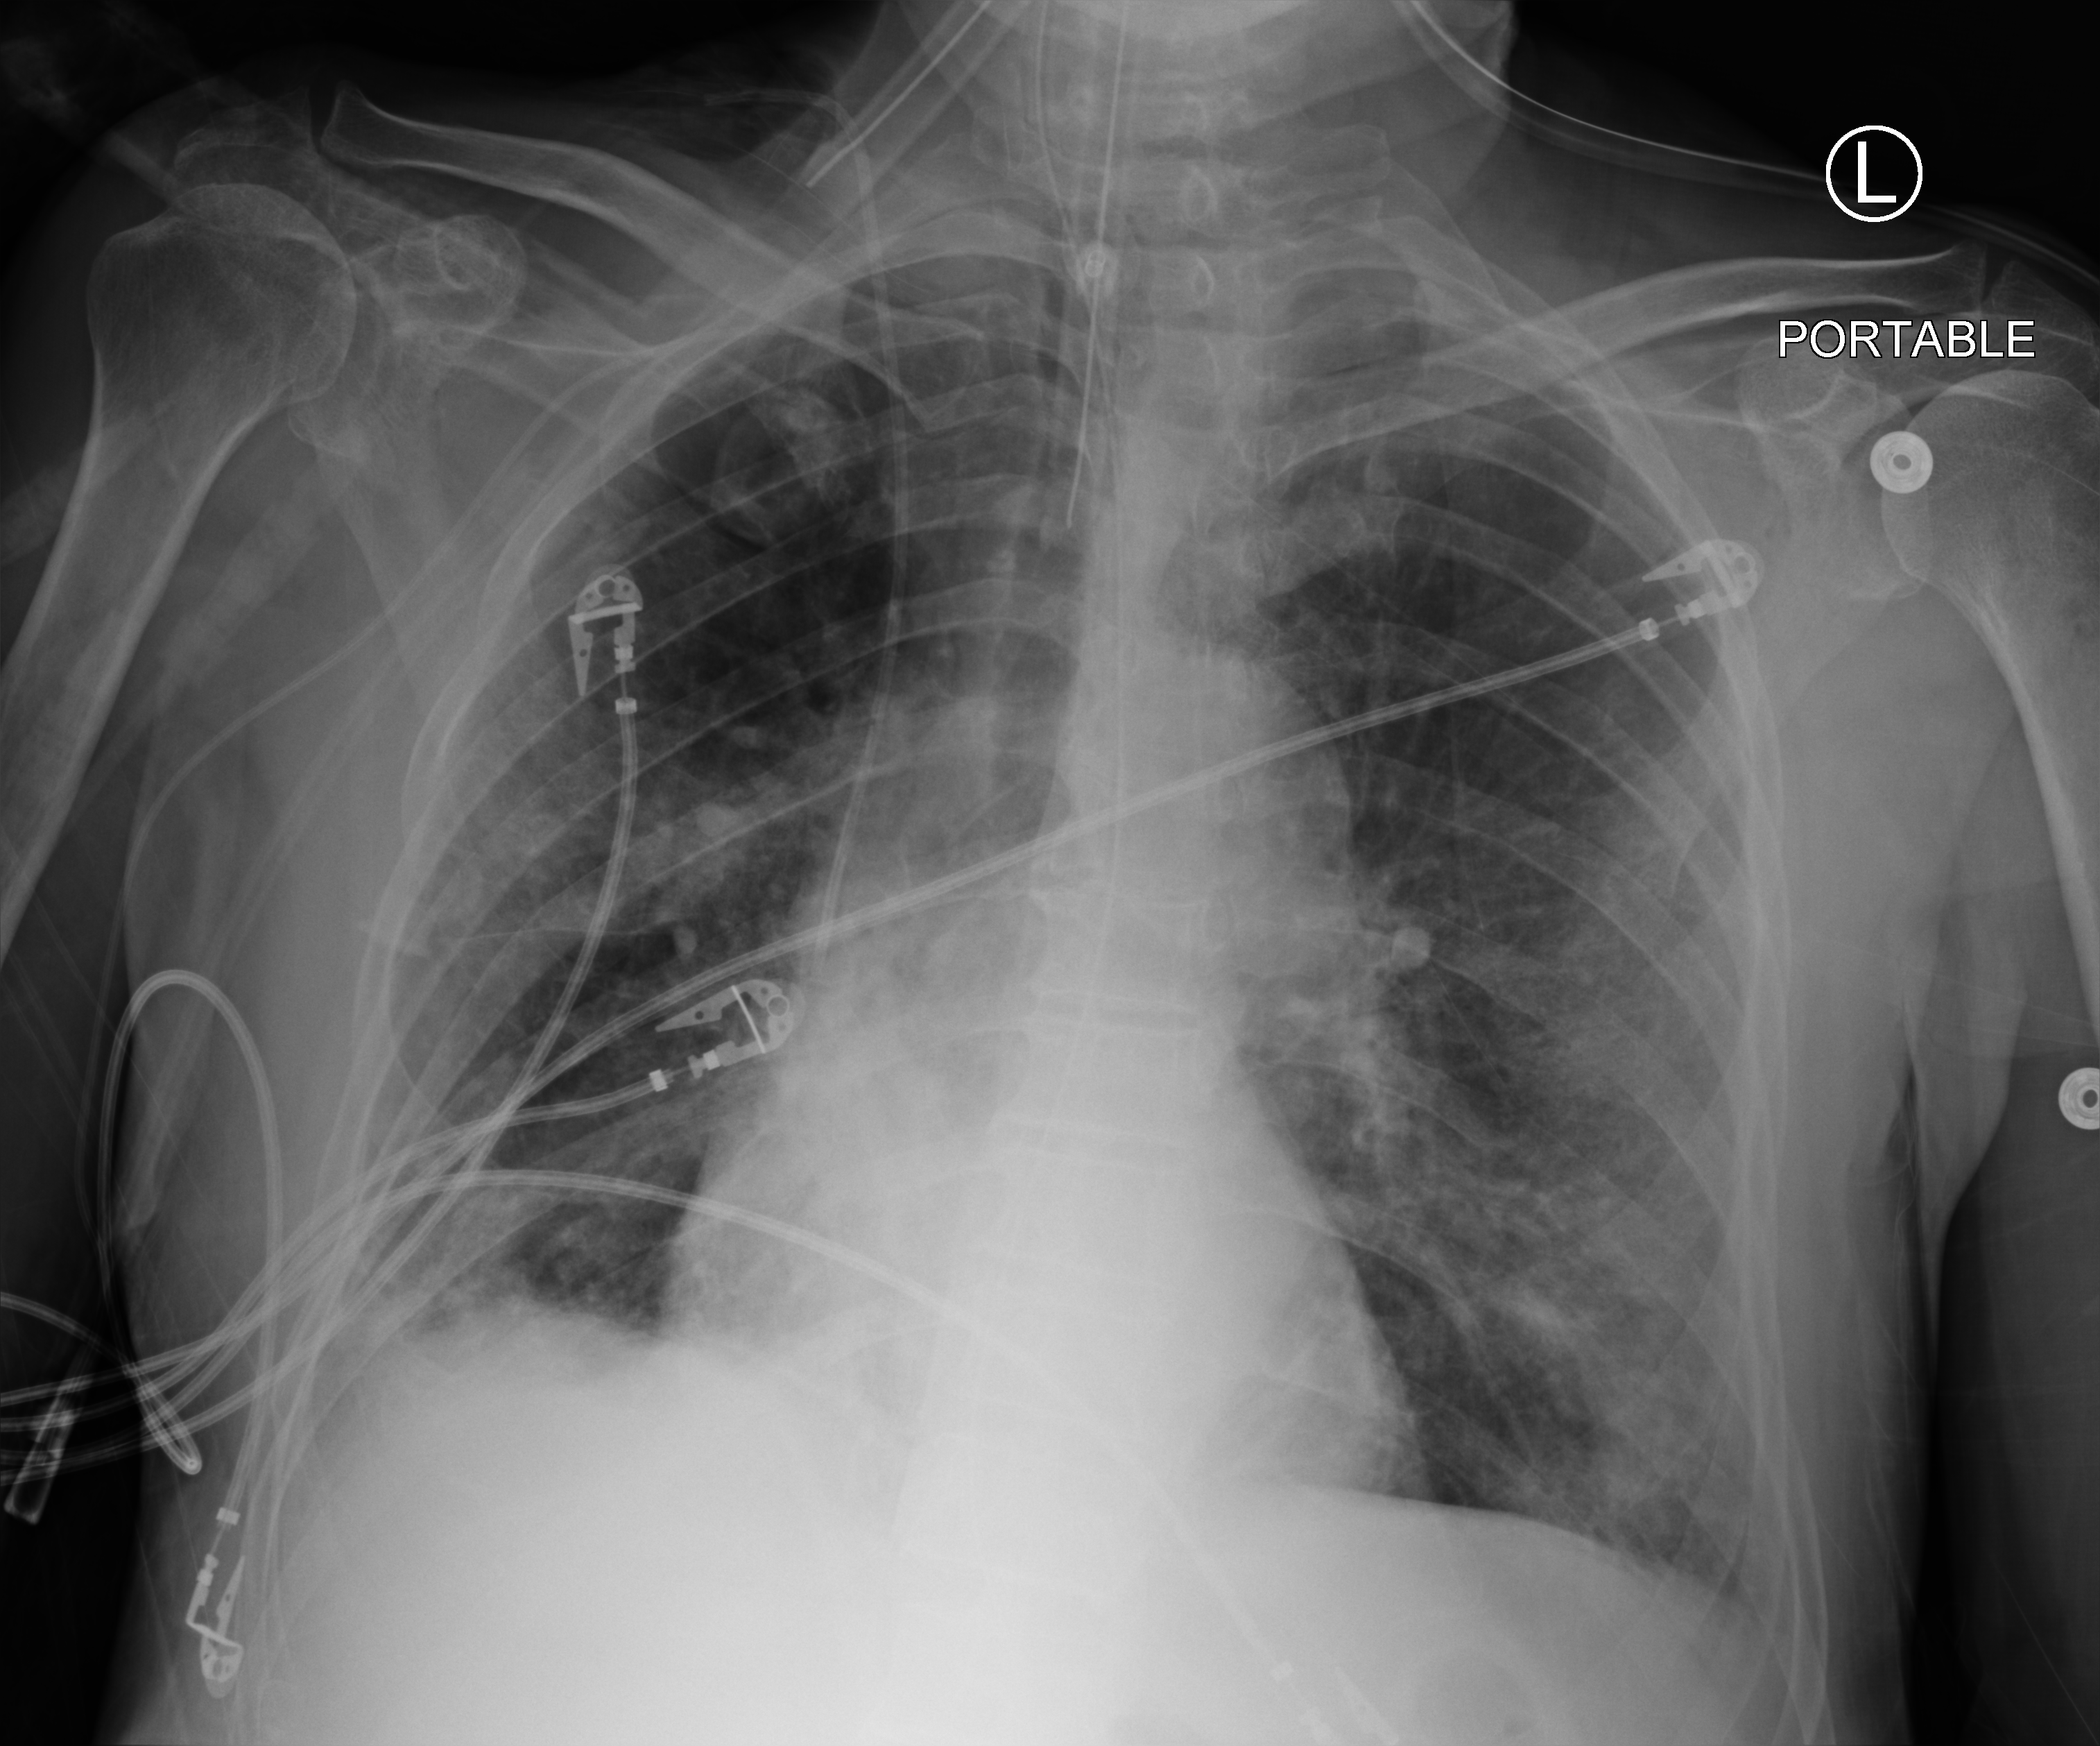
Chest X-ray (portable); anteroposterior (AP) projection. Patient hospitalised with COVID-19; male, aged 75–90 years.
From the hospital-stay record, not from the radiograph (when in the stay this image was taken is not recorded): smoking status (admission record): never; mechanically ventilated during this hospital stay: yes; admitted to intensive care during this hospital stay: yes.